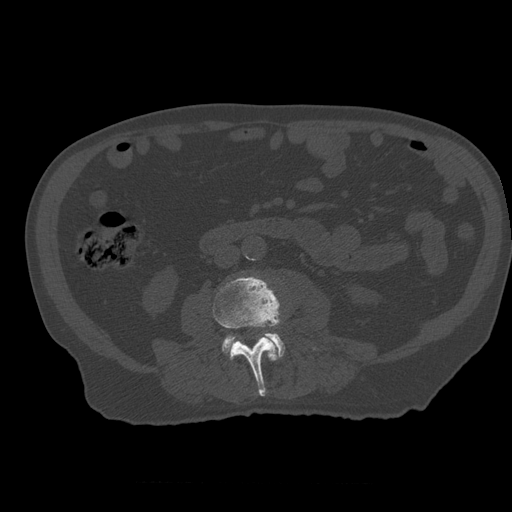
CT including the spine, one axial slice; slice 183 of 399 in the series (ordered by position); reconstruction kernel STANDARD; 120 kVp; bone window (W 1800 / L 400 HU); 512 × 512 image matrix. Patient age 73 years. From the clinical record (not read from this slice): primary cancer: prostate; vertebrae with lytic lesions (as recorded): L2.
Structures marked on this image (semi-automatic segmentation, software-assisted and operator-edited):
- L3 vertebra: box from (x=213, y=277) to (x=316, y=397) px
- L4 vertebra: (x=222, y=334)–(x=285, y=357)